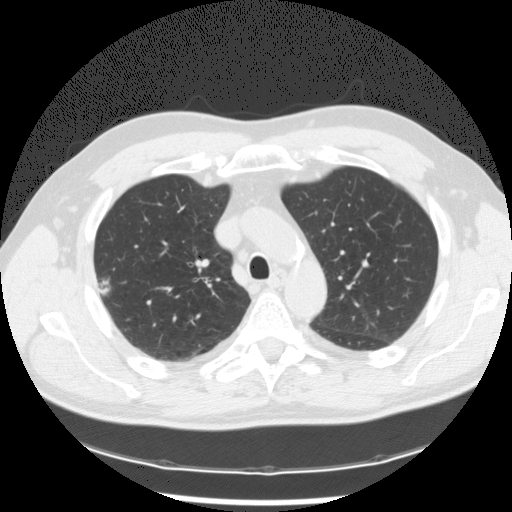
Axial slice from a low-dose chest CT screening exam, baseline annual screen, lung window (W 1500 / L -600 HU), 2.5 mm slice thickness. Male participant, aged 62 years at enrolment. Former smoker at enrolment.
Lesion marked by an expert reader, bounding box <89,271,118,301> (left, top, right, bottom; pixels). Reader record for this screening exam (exam-level; its link to the box is not recorded): non-calcified nodule or mass ≥4 mm, right upper lobe, 14 × 11 mm, poorly defined margins, mixed attenuation.